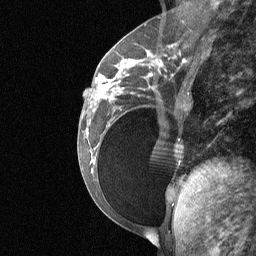
Breast MRI (dynamic contrast-enhanced), one sagittal slice; slice 26 of 64 in the series (ordered by position); dynamic contrast-enhanced study with each time point stored as its own series, time point 2 of 3 at this slice position (early post-contrast, ordered by acquisition time); 1.5 T; TE 4.8 ms, TR 27 ms; 2 mm slice thickness; 256 × 256 image matrix. Patient: female, 34 years. From the clinical record (not read from this slice): setting: breast cancer imaged before/during neoadjuvant chemotherapy; receptor status: HR-positive, HER2-negative.
Outlined on this slice (semi-automatic segmentation, software-assisted and operator-edited):
- analysis volume of interest (the breast-tissue region the enhancement analysis was run in; not a lesion): bounding box (x1, y1, x2, y2) in pixels: (92, 50, 188, 185)
- tumour enhancement mask (voxels above the 90 % enhancement threshold inside the analysis volume of interest): (96, 64, 132, 100)